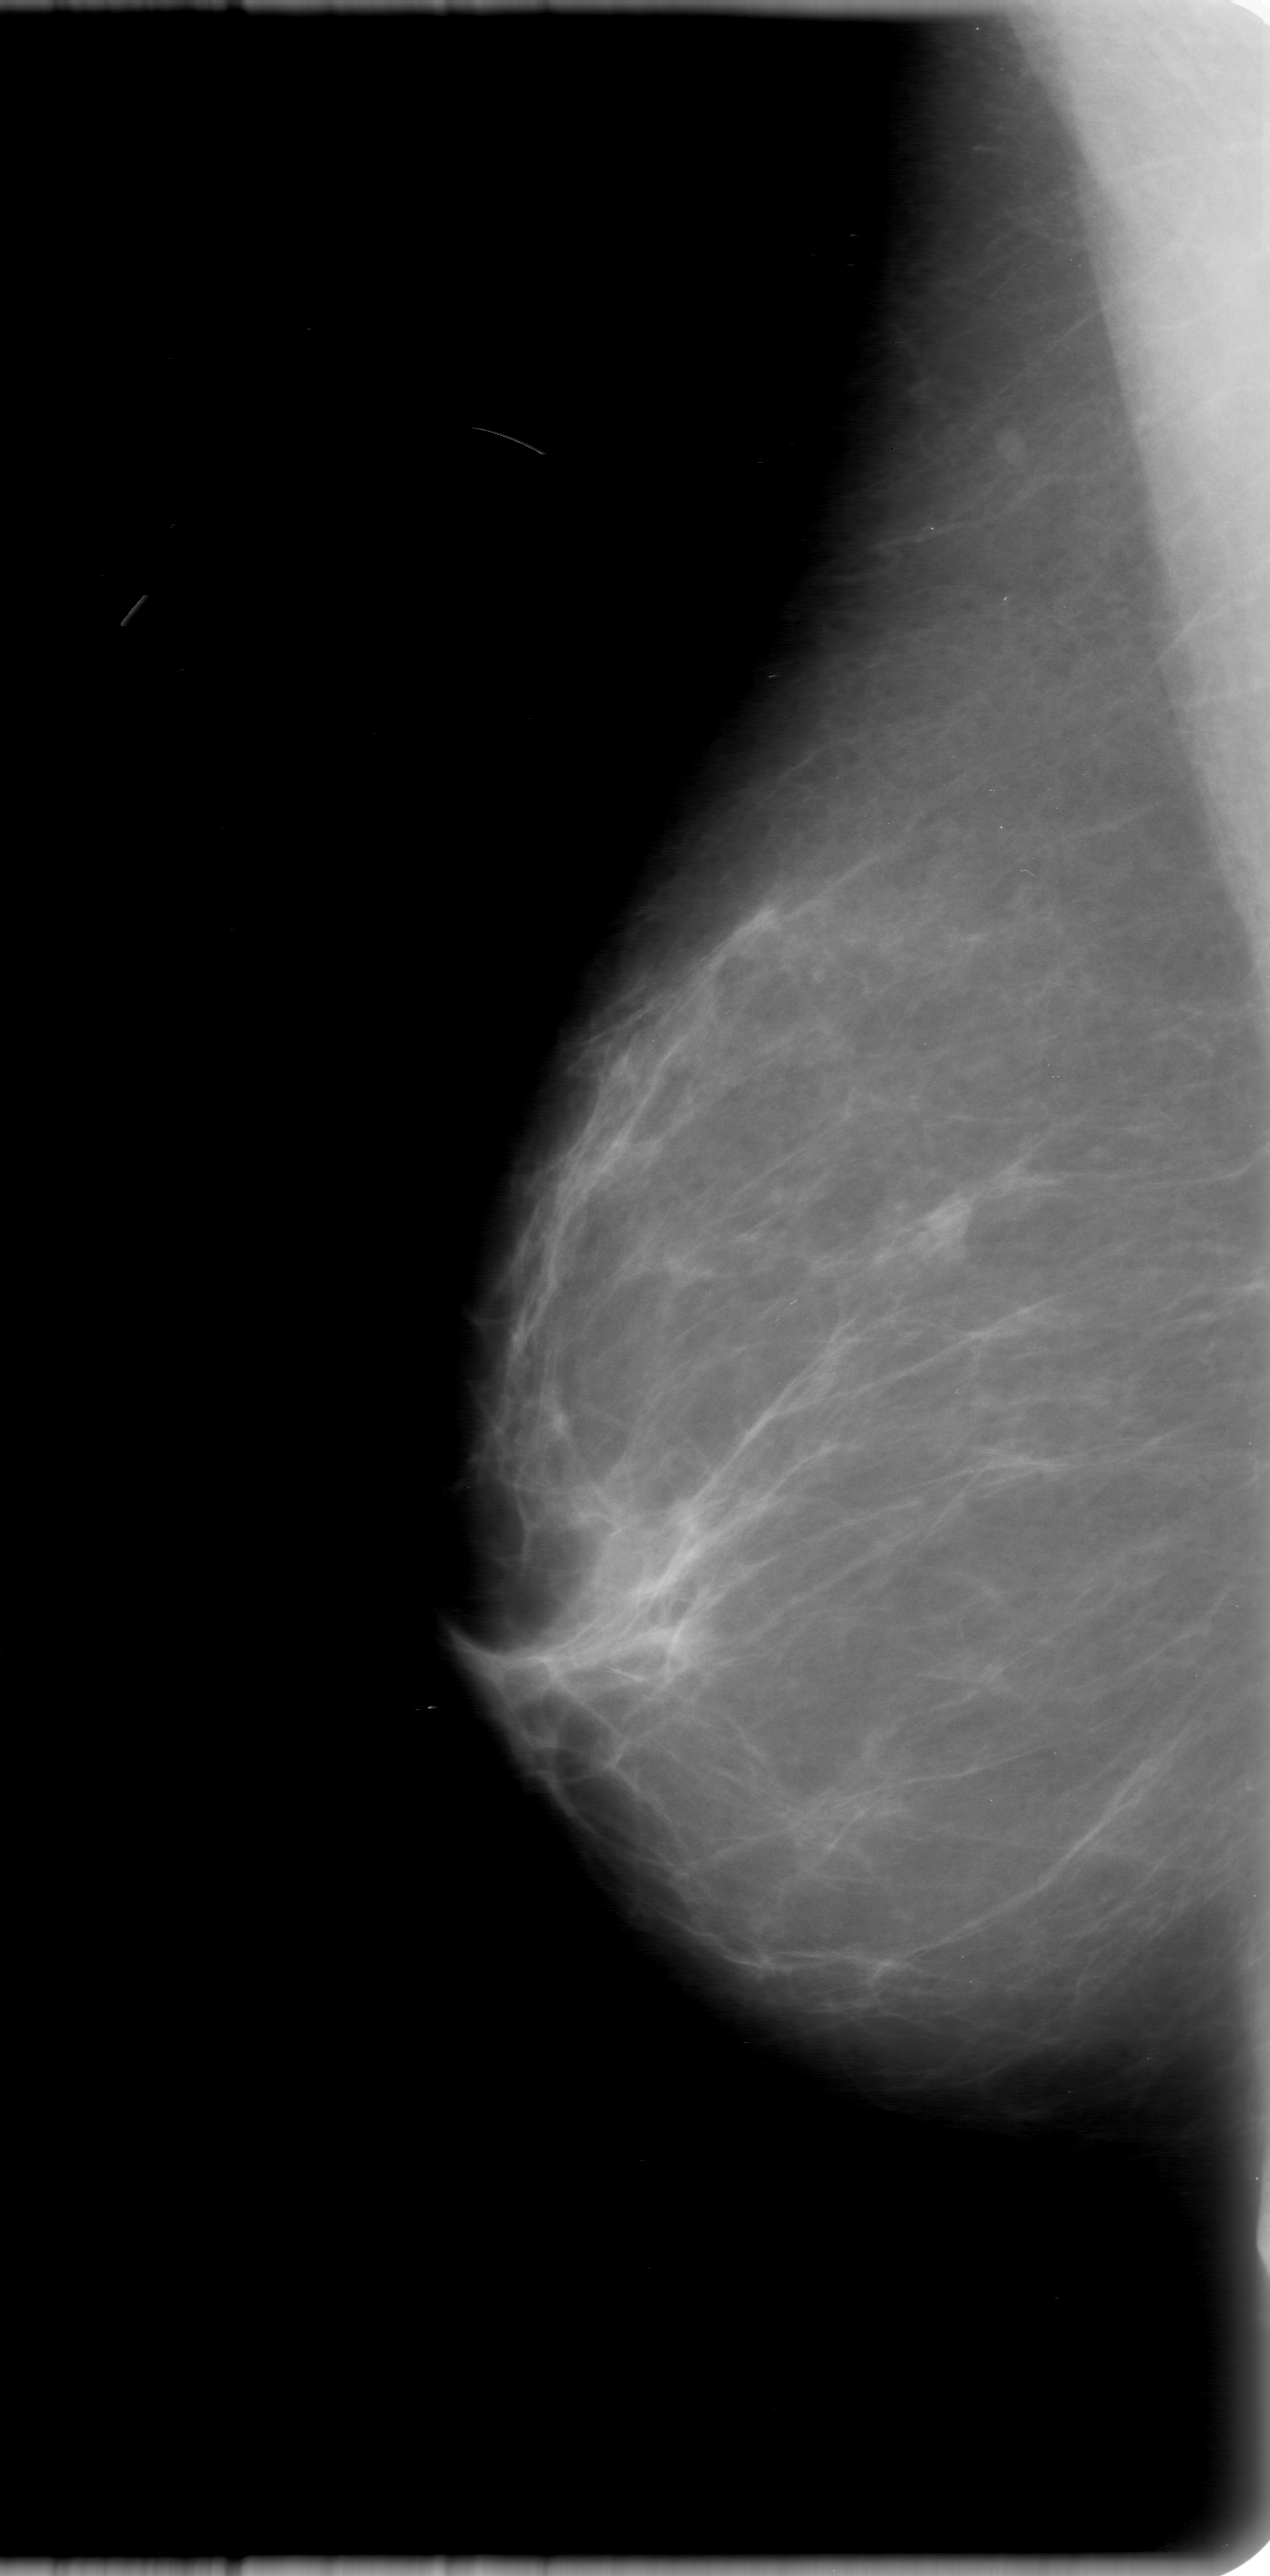
Scanned film-screen mammogram; right breast; mediolateral oblique (MLO) view; BI-RADS breast density category 1 (scale 1–4).
Finding: mass, shape lobulated, margins obscured; BI-RADS assessment category 0; subtlety rating 4 on a 1 (subtle) to 5 (obvious) scale; pathology (as recorded): benign.